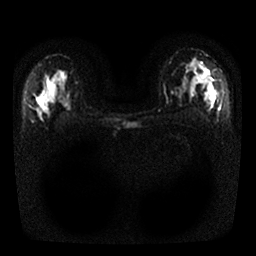
Breast MRI, one axial slice; diffusion-weighted series; image 2 of 4 stored at this slice position (different b-values; order by instance number); 1.5 T; 4 mm slice thickness; 256 × 256 image matrix, field of view 320 × 320 mm. Female patient.
Structures marked on this image (outlined manually by an expert reader):
- tumour on diffusion-weighted imaging: bounding box [x1, y1, x2, y2] px = [197, 70, 213, 98]